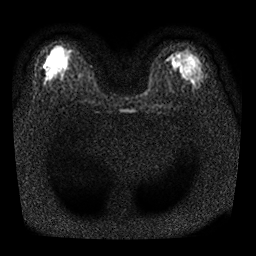
Breast MRI, one axial slice; position 17 of 25 along the scan axis; diffusion-weighted series; image 2 of 4 stored at this slice position (different b-values; order by instance number); 1.5 T; 4 mm slice thickness; 256 × 256 image matrix, field of view 310 × 310 mm. Female patient.
Structures marked on this image (expert manual segmentation):
- tumour on diffusion-weighted imaging: bounding box (x1, y1, x2, y2) in pixels: (45, 61, 51, 69)